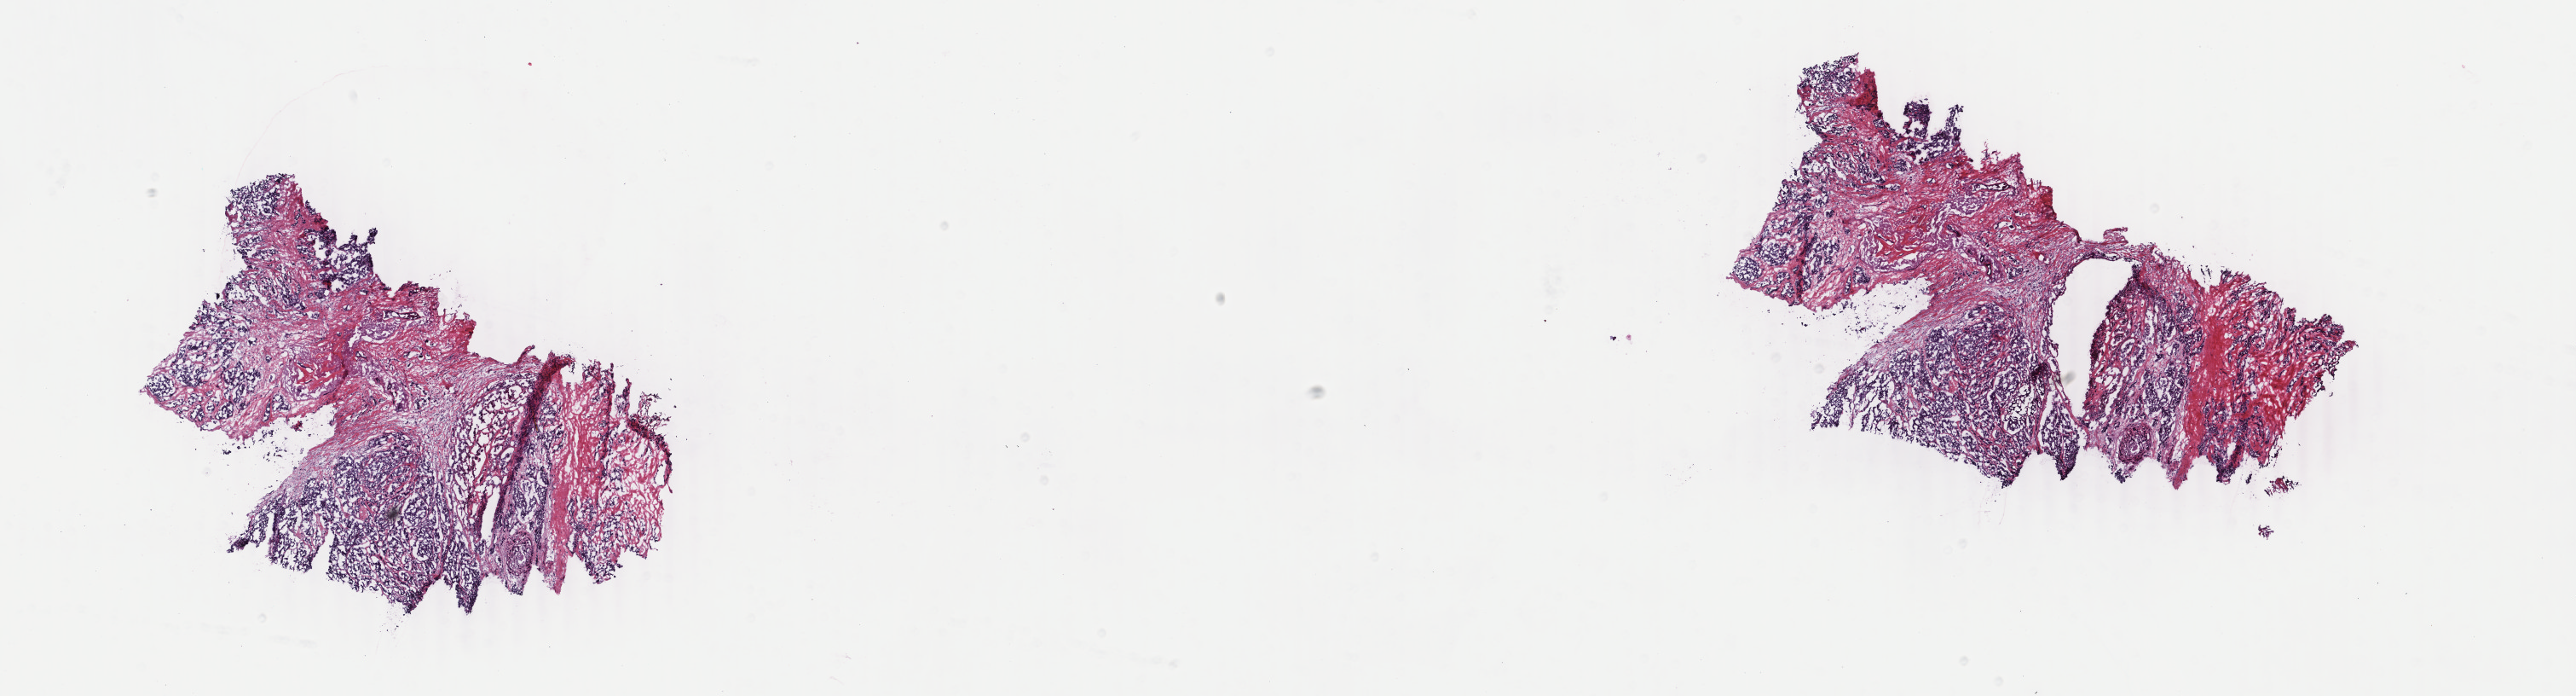
Digitized H&E-stained tissue section (whole slide), a low-resolution overview of the entire scanned area, about 24.0 x 6.5 mm (acquisition: 40x scan). Frozen section from the top of the tissue portion. Sample: primary tumour, breast. Female, age 66 years at initial diagnosis. Slide review estimates, as recorded: tumour cells 75%, tumour nuclei 75%, normal cells 0%, stromal cells 19%, necrosis 6%. Inflammatory infiltration, as recorded: lymphocyte infiltration 1%, monocyte infiltration 0%, neutrophil infiltration 0%.
* lymph nodes positive (case pathology): 0 of 17 examined
* histologic diagnosis: Infiltrating duct carcinoma, NOS
* AJCC pathologic stage: IIA
* laterality: left